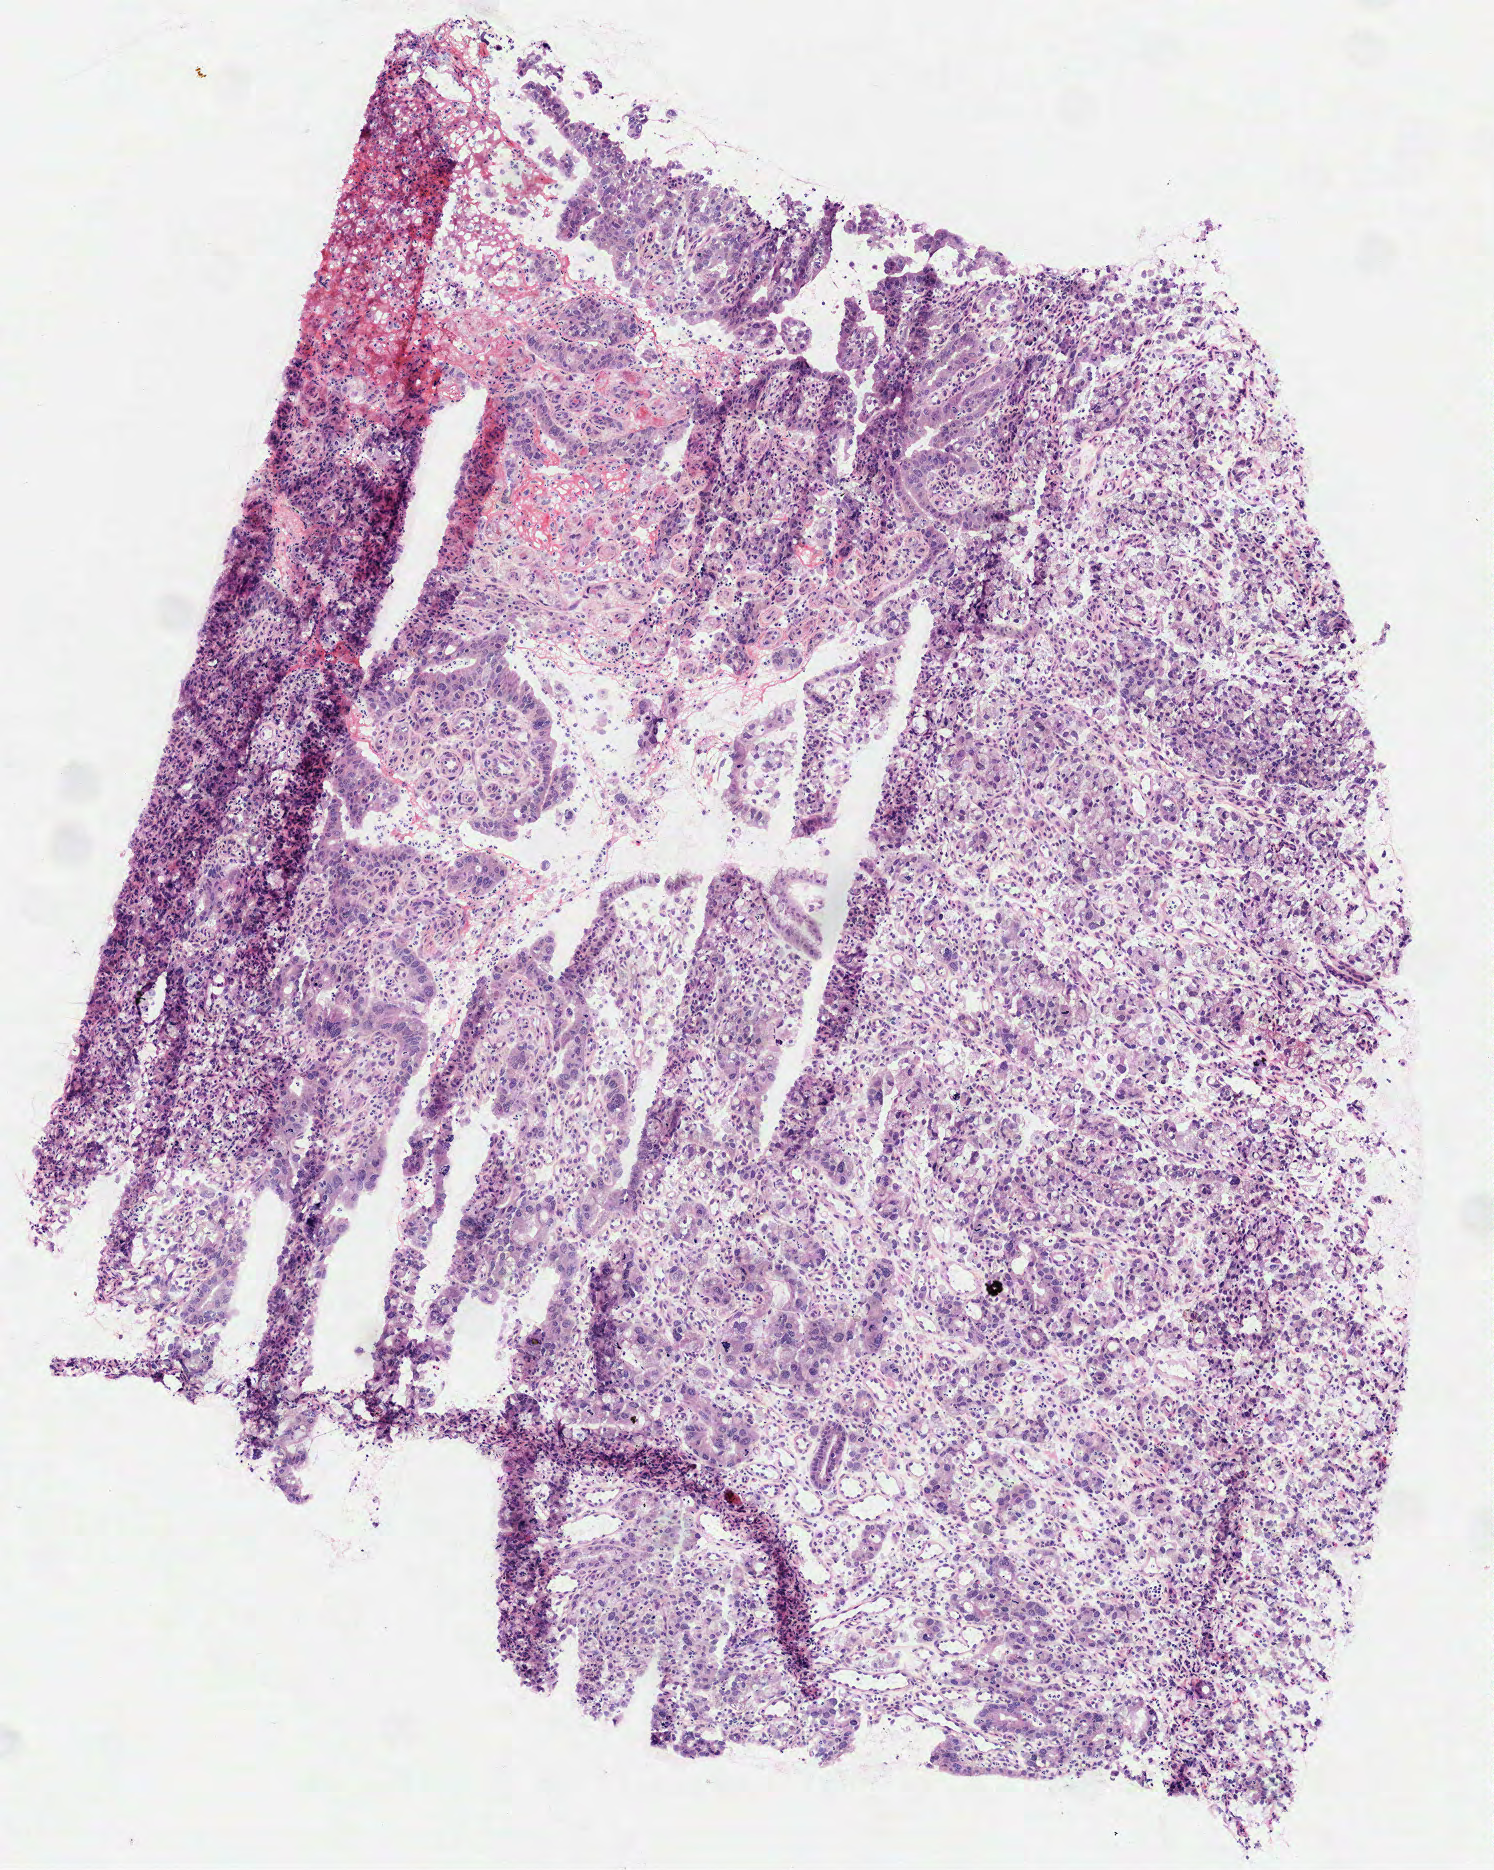
Whole-slide histology image, H&E-stained — shown as a low-resolution overview of the whole scanned area (about 3.0 x 3.8 mm); frozen section; primary tumour sample from the stomach. Patient: female, age at initial diagnosis 54 years. Histologic grade: G3 (poorly differentiated). Composition of this section per pathologist review: tumour cells 100%, tumour nuclei 75%, normal cells 0%, stromal cells 0%, necrosis 0%. Inflammatory infiltration, as recorded: lymphocyte infiltration 5%, monocyte infiltration 5%, neutrophil infiltration 5%.
AJCC pathologic stage: IIIB. Histologic diagnosis: Tubular adenocarcinoma (gastric antrum). TNM: T3 N3a M0. Lymph nodes positive (case pathology): 15 of 15 examined.